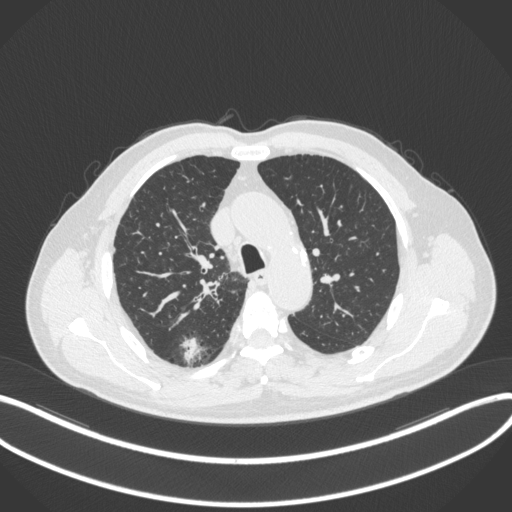
Chest CT, one axial slice. Slice 268 of 366 in the series (ordered by position). 120 kVp. Lung window (W 1500 / L -600 HU). 1 mm slice thickness. 512 × 512 image matrix, field of view 400 × 400 mm. Male patient, age 69 years. Case-level facts recorded for this patient, not image findings: clinical TNM (as recorded): T1b N0 M0; histopathological grade: G2-3.
Annotated regions visible in this slice (bounding box drawn by a radiologist):
- lung tumour (recorded histology: adenocarcinoma): bounding box [x1, y1, x2, y2] px = [181, 333, 202, 366]